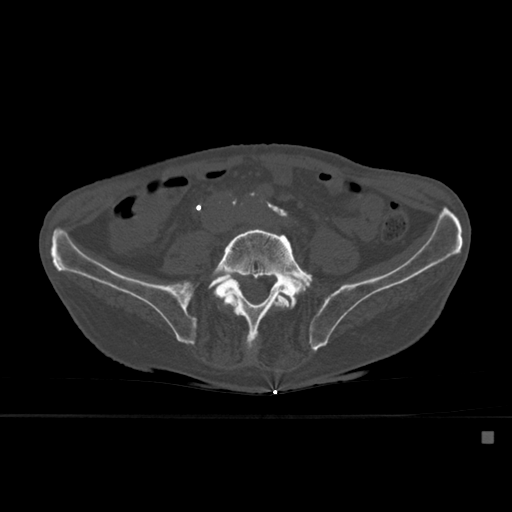
CT including the spine, one axial slice; slice 178 of 527 in the series (ordered by position); bone window (W 1800 / L 400 HU); 512 × 512 image matrix, field of view 373 × 373 mm. Patient: male, 78 years. From the clinical record (not read from this slice): primary cancer: prostate.
Outlined on this slice (semi-automatic segmentation, software-assisted and operator-edited):
- L4 vertebra: bounding box <222,292,294,353> (left, top, right, bottom; pixels)
- L5 vertebra: <210,227,314,352>